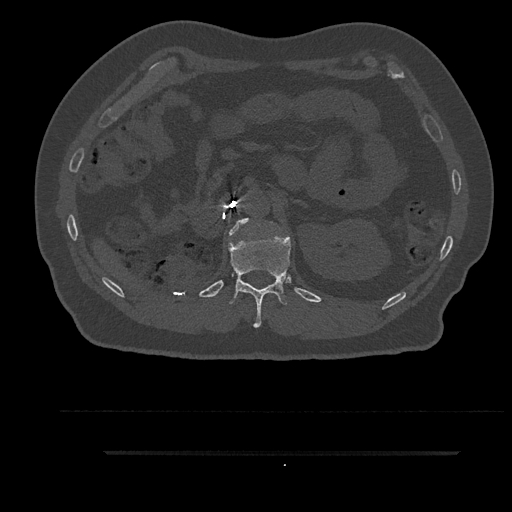
CT including the spine, one axial slice; slice 230 of 797 in the series (ordered by position); reconstruction kernel Br40s/3; bone window (W 1800 / L 400 HU); 0.5 mm slice thickness; 512 × 512 image matrix. Patient: male, 63 years. From the clinical record (not read from this slice): primary cancer: renal; vertebrae with lytic lesions (as recorded): T8.
Outlined on this slice (semi-automatic segmentation, software-assisted and operator-edited):
- L1 vertebra: box from (x=229, y=218) to (x=249, y=235) px
- T12 vertebra: (x=228, y=230)–(x=291, y=328)